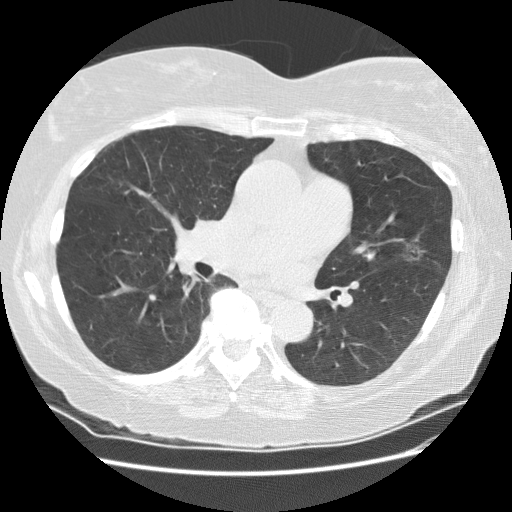
Low-dose screening chest CT, axial slice; second annual screen; lung window (W 1500 / L -600 HU); 2.5 mm slice thickness; standard (soft-tissue) reconstruction kernel (STANDARD); 120 kVp; slice 97 of 180 in the series. Female participant, aged 71 years at enrolment. Former smoker at enrolment.
Lesion marked by an expert reader, bounding box <388,225,439,267> (left, top, right, bottom; pixels). Screening reader's record for this exam (one nodule recorded; not confirmed to be the boxed lesion): non-calcified nodule or mass ≥4 mm, lingula, 13 × 13 mm, poorly defined margins, ground glass attenuation, pre-existing on the prior screen: yes; interval growth: yes.